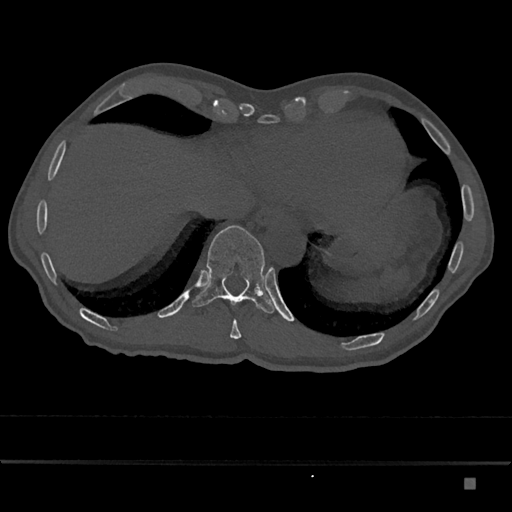
CT including the spine, one axial slice. Slice 694 of 797 in the series (ordered by position). Bone window (W 1800 / L 400 HU). 0.5 mm slice thickness. 512 × 512 image matrix, field of view 390 × 390 mm. Male patient, age 72 years. Case-level facts recorded for this patient, not image findings: primary cancer: prostate.
Structures marked on this image (semi-automatic segmentation, software-assisted and operator-edited):
- T10 vertebra: bounding box (x1, y1, x2, y2) in pixels: (230, 320, 242, 339)
- T11 vertebra: (192, 225, 274, 314)